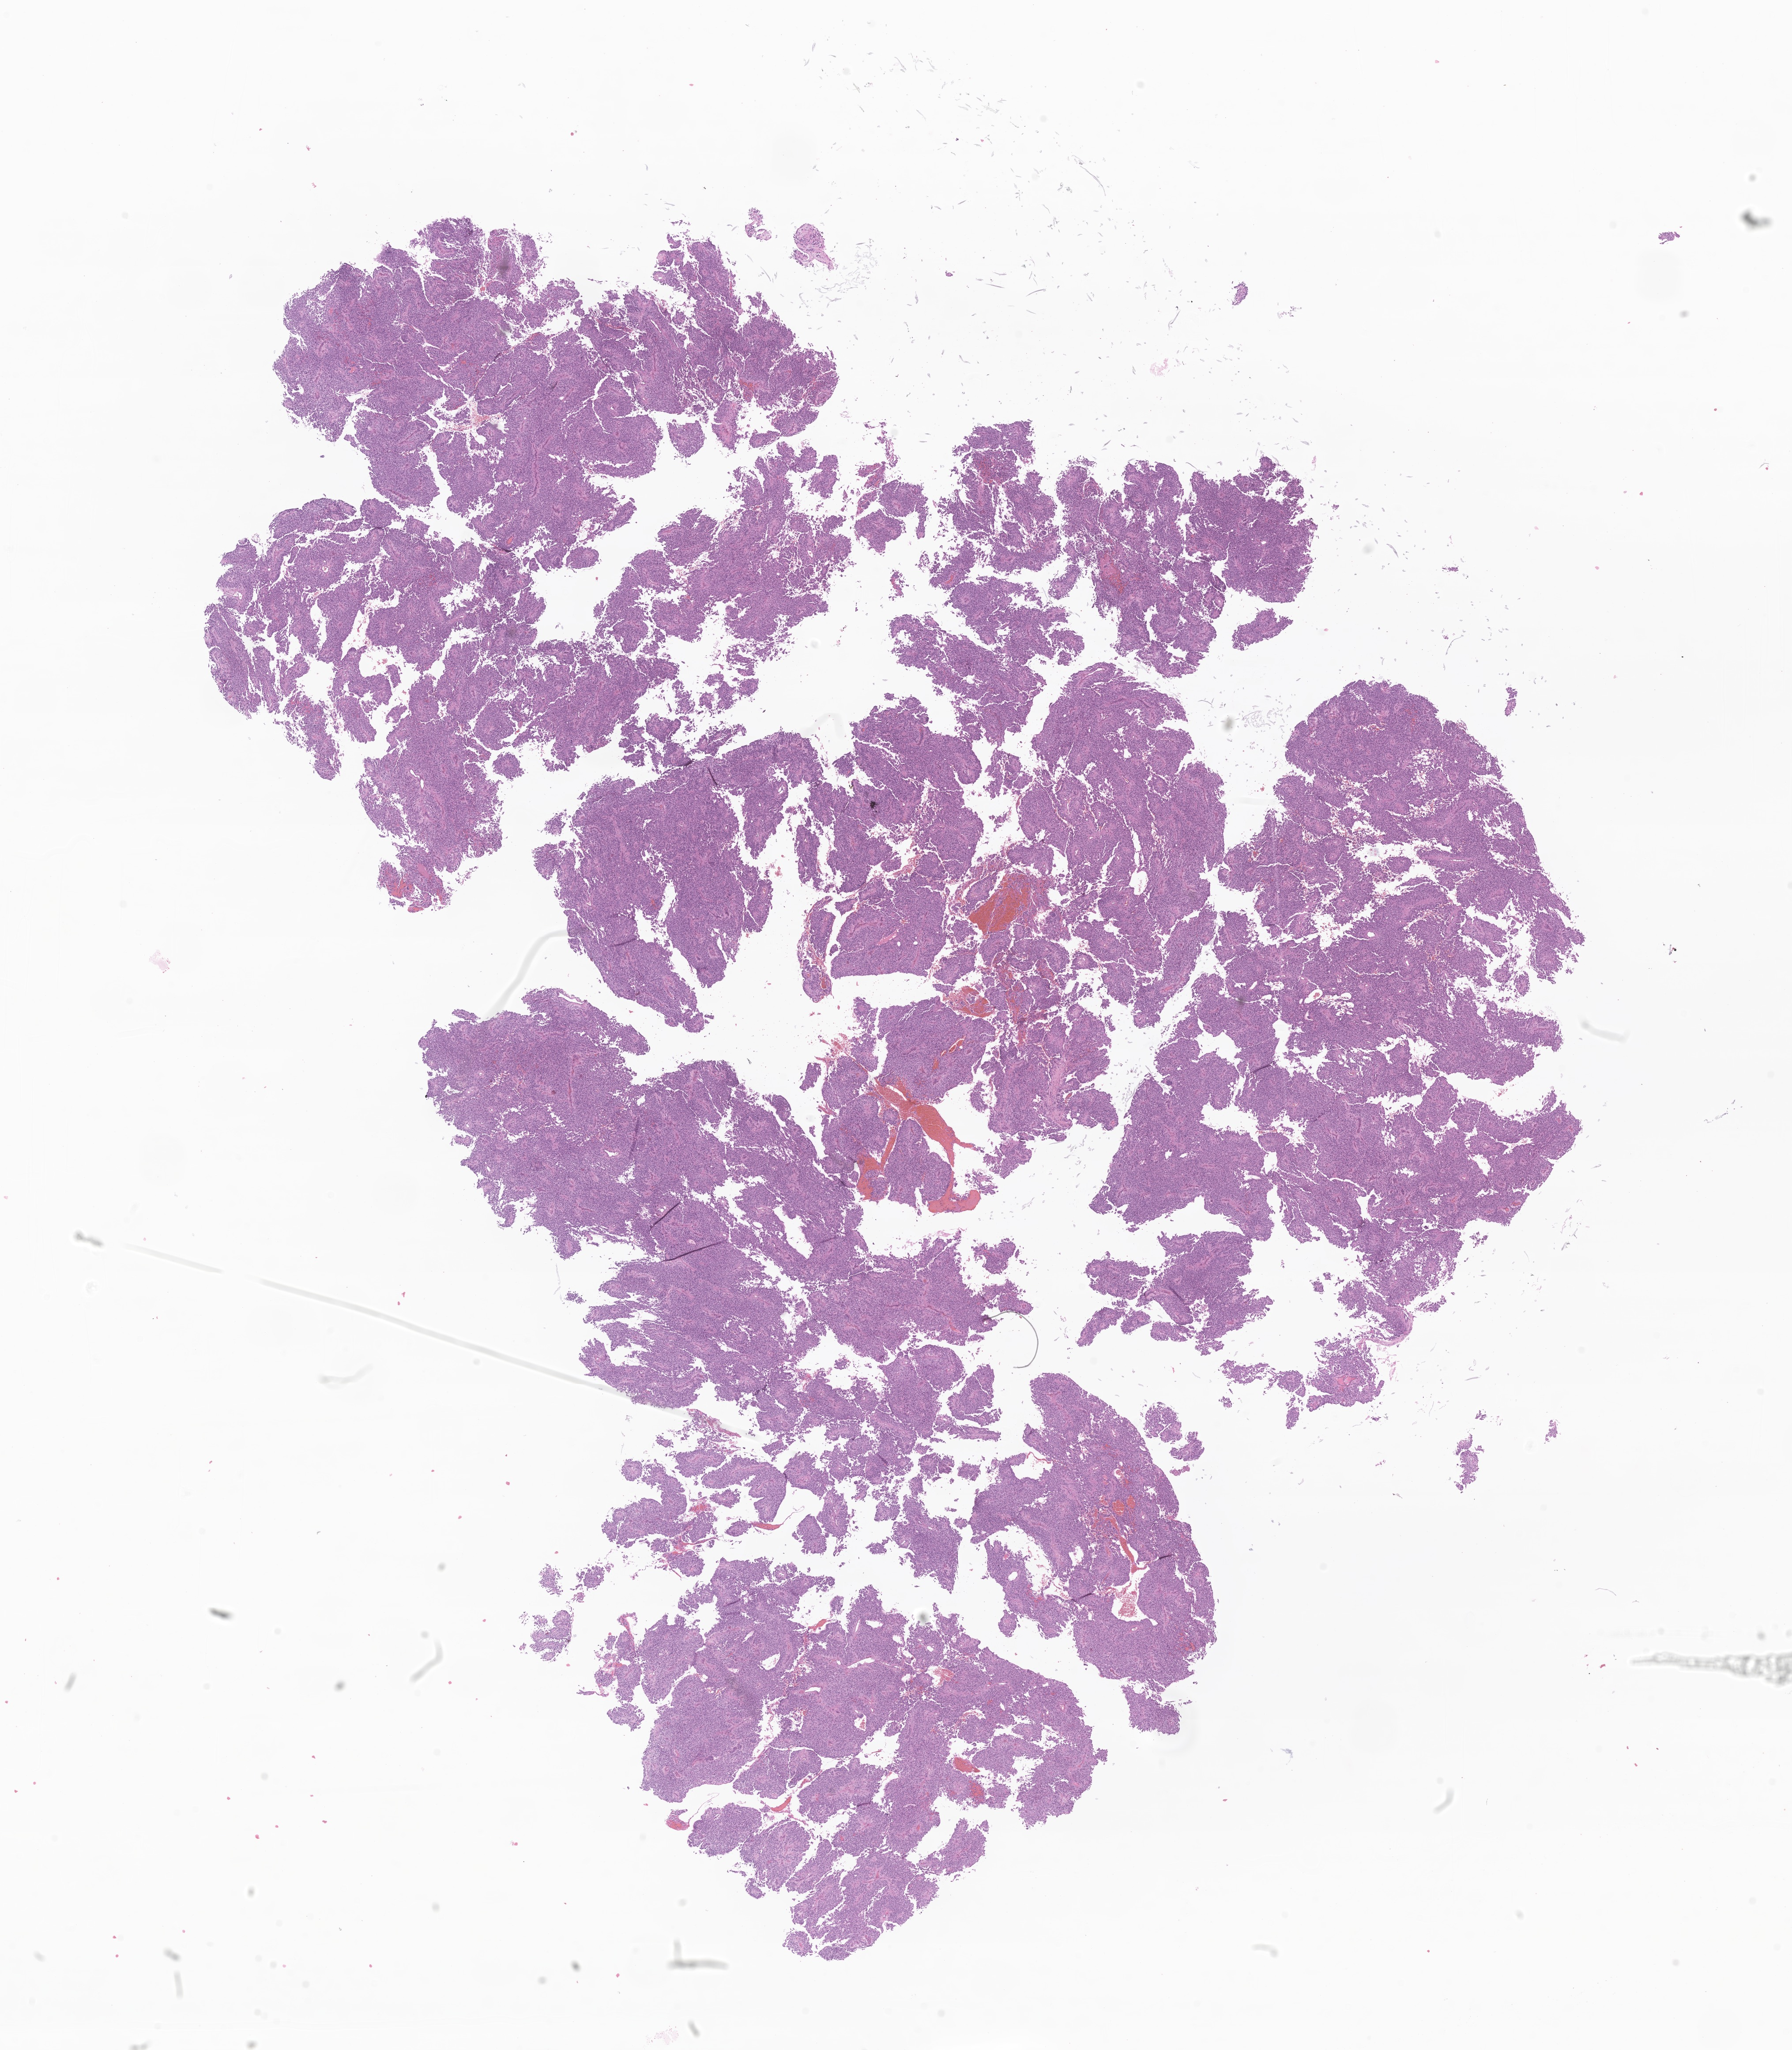
H&E whole-slide image of tumor tissue from the spinal cord, shown as a low-resolution overview of the whole scanned area (about 17.1 x 19.6 mm). FFPE section. Male patient, age 115 months.
Recorded diagnosis: Ependymoma, NOS.